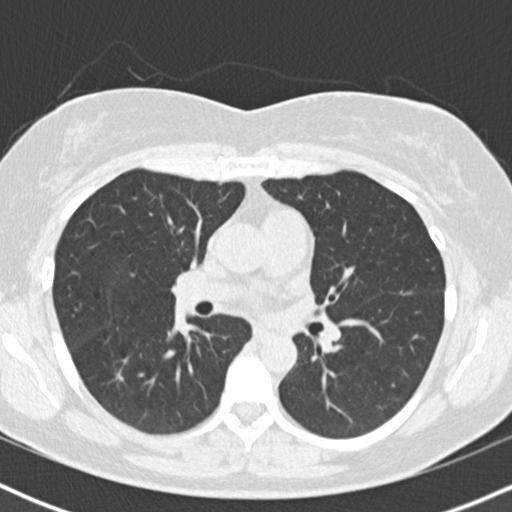
Low-dose screening chest CT, one axial slice. Position 96 of 167 along the scan axis. Reconstruction kernel B30f. 120 kVp. Lung window (W 1500 / L -600 HU). 2 mm slice thickness. 512 × 512 image matrix.
Structures marked on this image (manually delineated by an expert):
- lesion 1 (tumor, lower lobe of right lung): box from (x=116, y=370) to (x=124, y=381) px